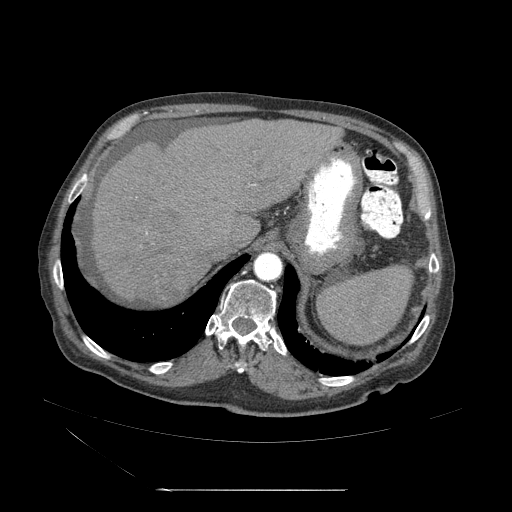
Contrast-enhanced abdominal CT (liver protocol), one axial slice. Slice 40 of 71 in the series (ordered by position). Reconstruction kernel STANDARD. 120 kVp. Soft-tissue window (W 400 / L 40 HU). 2.5 mm slice thickness. 512 × 512 image matrix, field of view 440 × 440 mm. From the clinical record (not read from this slice): diagnosis: hepatocellular carcinoma (patient treated with transarterial chemoembolisation; whether this scan precedes or follows treatment is not stated here); TNM stage (as recorded): Stage-II; Child-Pugh class: A; tumour nodularity: multinodular; tumour size: 1 cm.
Structures marked on this image (semi-automatic segmentation, software-assisted and operator-edited):
- abdominal aorta: bounding box (x1, y1, x2, y2) in pixels: (254, 253, 284, 283)
- liver parenchyma outside the tumour (the mass and vessels are separate outlines, so this box may not span the whole liver): (88, 121, 344, 313)
- mass: (146, 268, 189, 309)
- liver vessels: (124, 199, 232, 265)